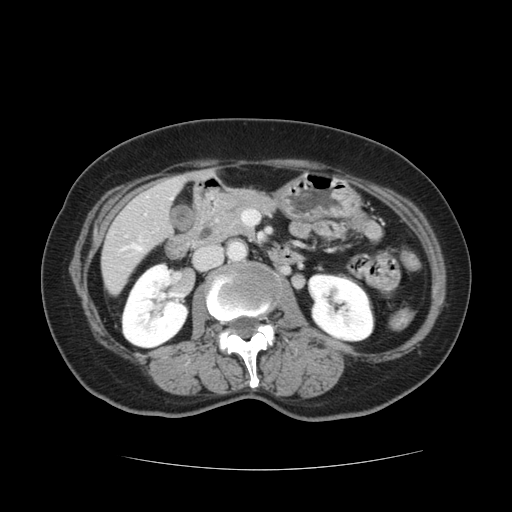
Contrast-enhanced abdominal CT, one axial slice. Slice 42 of 128 in the series (ordered by position). 120 kVp. Intravenous contrast given. Soft-tissue window (W 400 / L 40 HU). 2.5 mm slice thickness. 512 × 512 image matrix, field of view 366 × 366 mm. Female patient, age 67 years. Case-level facts recorded for this patient, not image findings: diagnosis: colorectal cancer liver metastases, imaged before liver resection; multiple liver metastases: yes; largest metastasis: 3 cm; disease in both lobes: yes.
Structures marked on this image (manually delineated by an expert):
- hepatic veins: bounding box <134,246,142,251> (left, top, right, bottom; pixels)
- liver: <102,176,184,293>
- planned liver remnant (the part of the liver to remain after resection): <101,220,159,293>